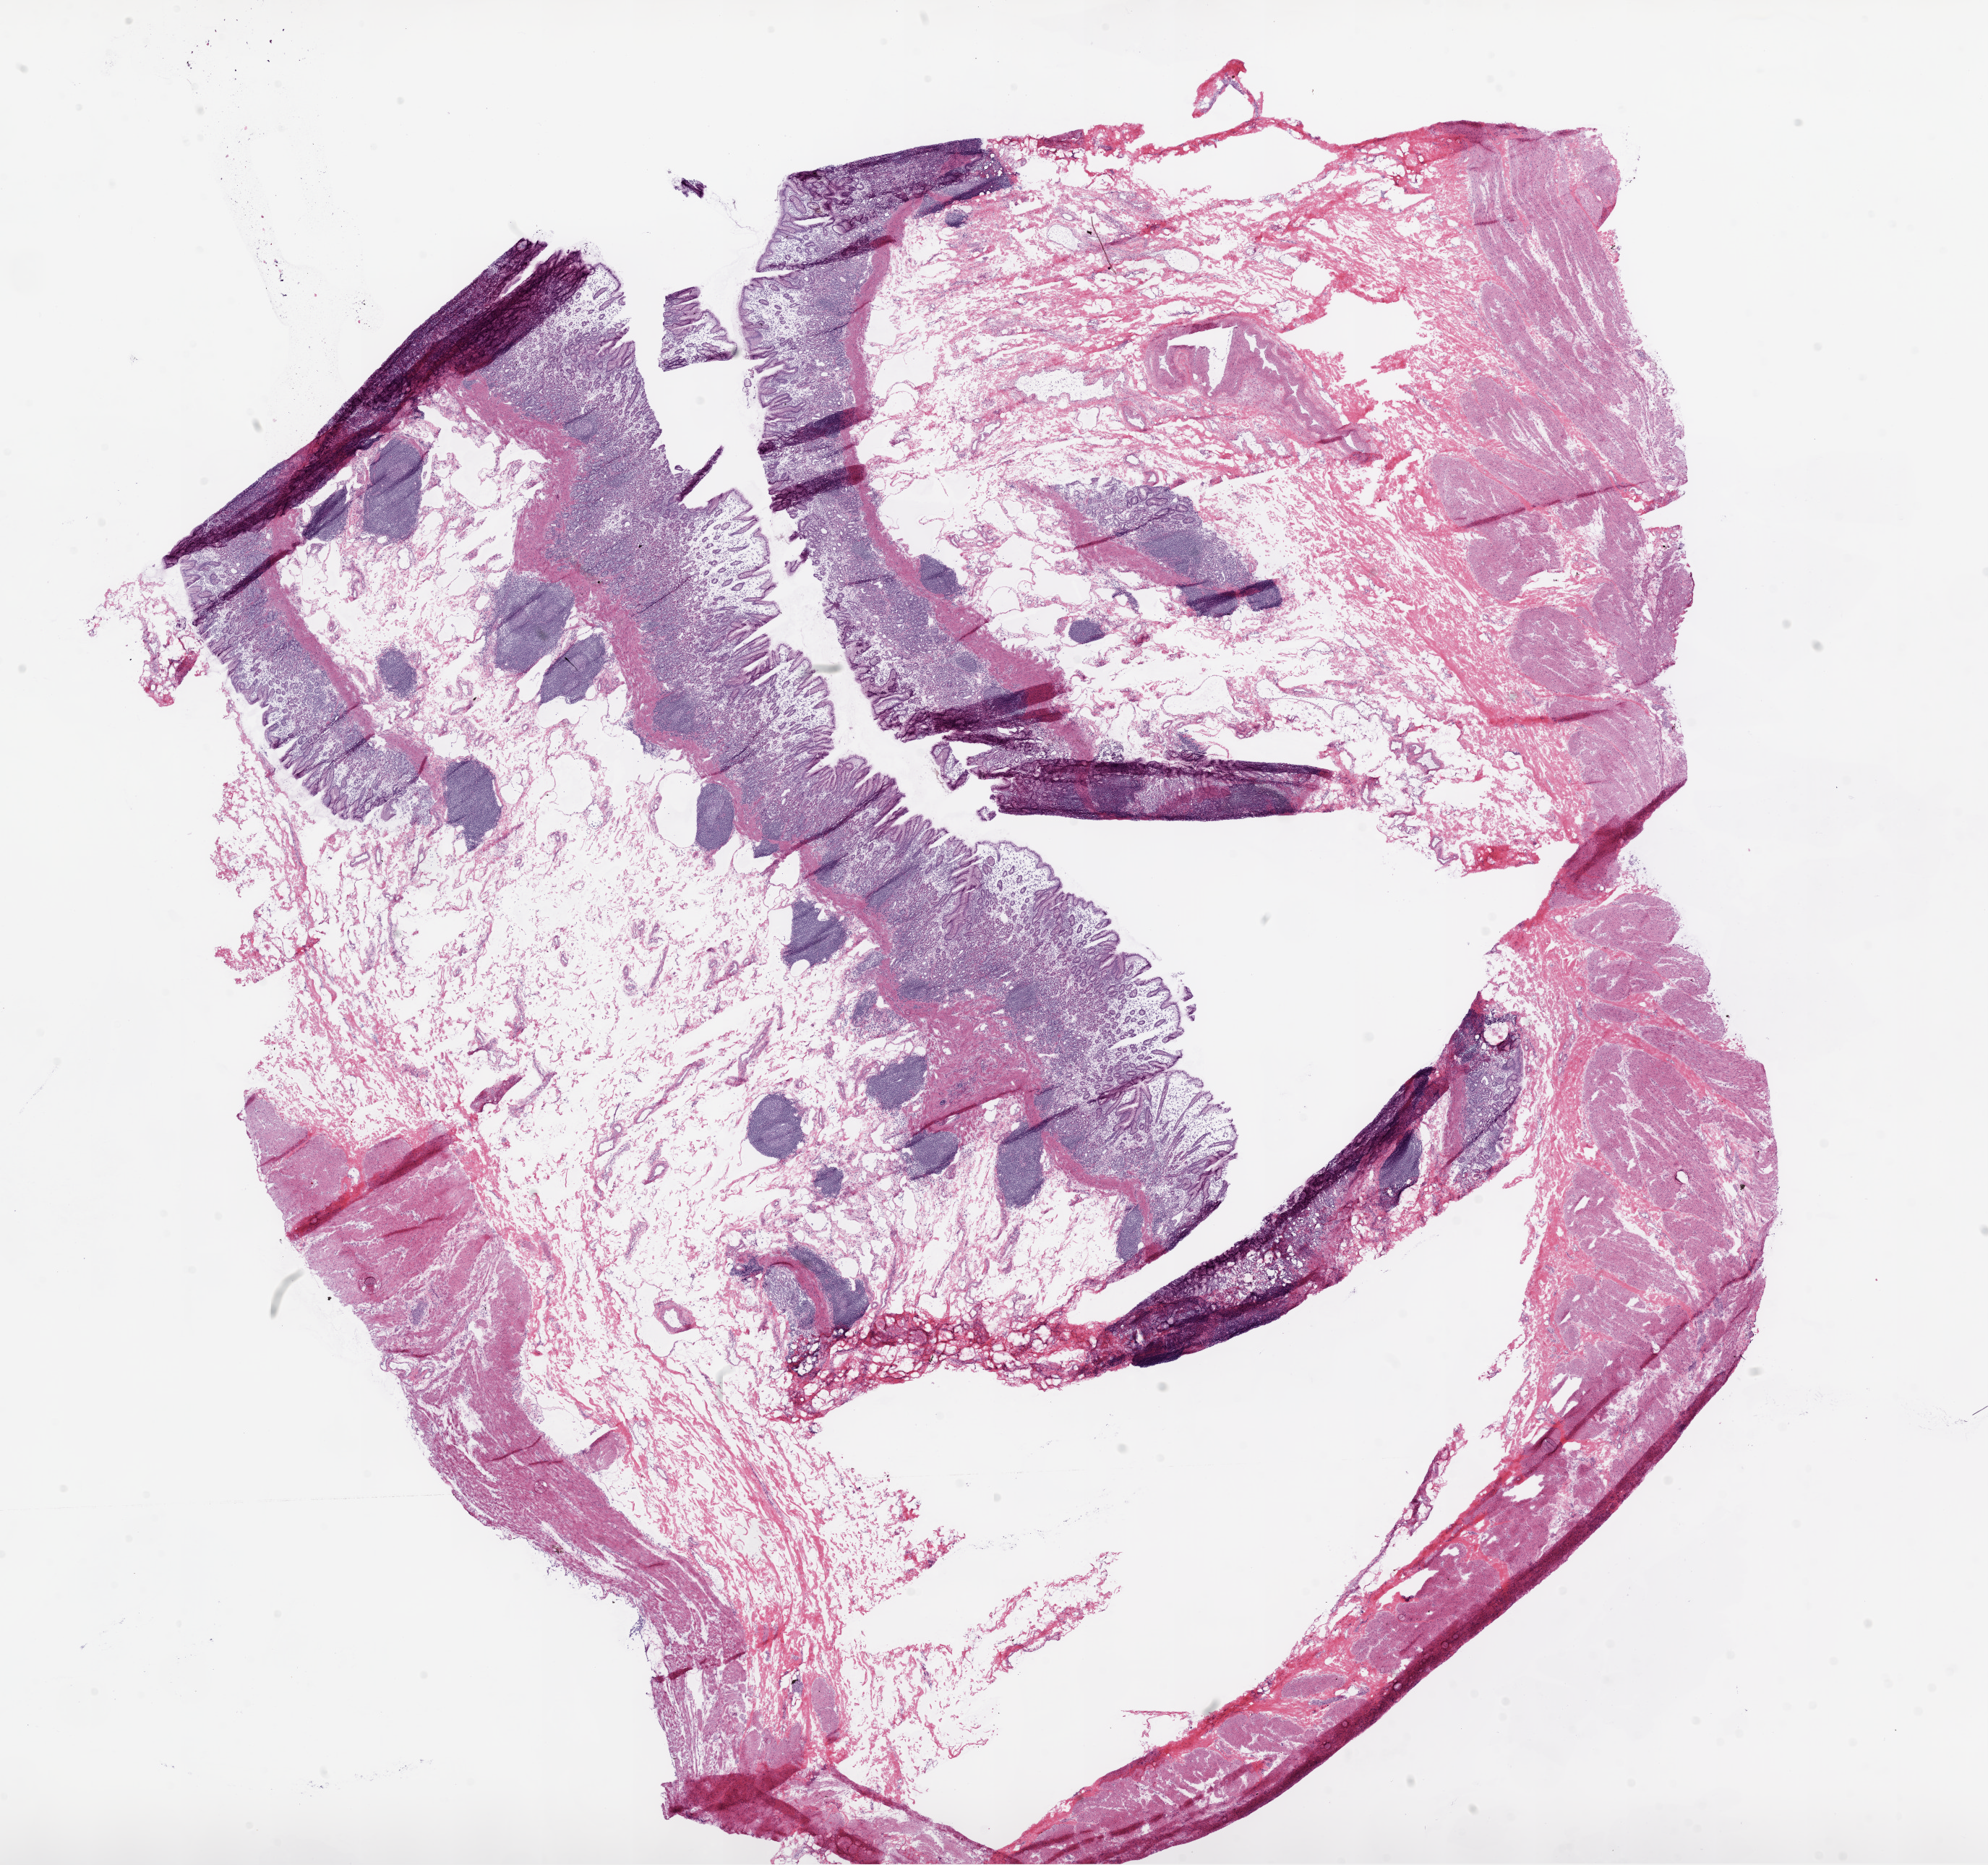
Whole-slide histology image, Hematoxylin and eosin (H&E) stained, shown as a low-resolution overview of the whole scanned area (about 22.1 x 20.7 mm, from a 20x scan). Frozen section from the top of the tissue portion. Stomach, solid tissue normal (non-tumour tissue) sample. Female, age 60 years at initial diagnosis.
This section: solid tissue normal sample (biorepository sample class). Patient diagnosis: Adenocarcinoma, NOS.